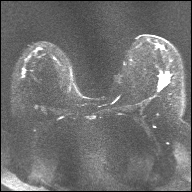
Breast MRI, one axial slice. Slice 18 of 32 in the series (ordered by position). Diffusion-weighted series; image 2 of 4 stored at this slice position (different b-values; order by instance number). 1.5 T. 4 mm slice thickness. 192 × 192 image matrix. Female patient.
Outlined on this slice (manually delineated by an expert):
- tumour on diffusion-weighted imaging: bounding box <160,76,168,88> (left, top, right, bottom; pixels)